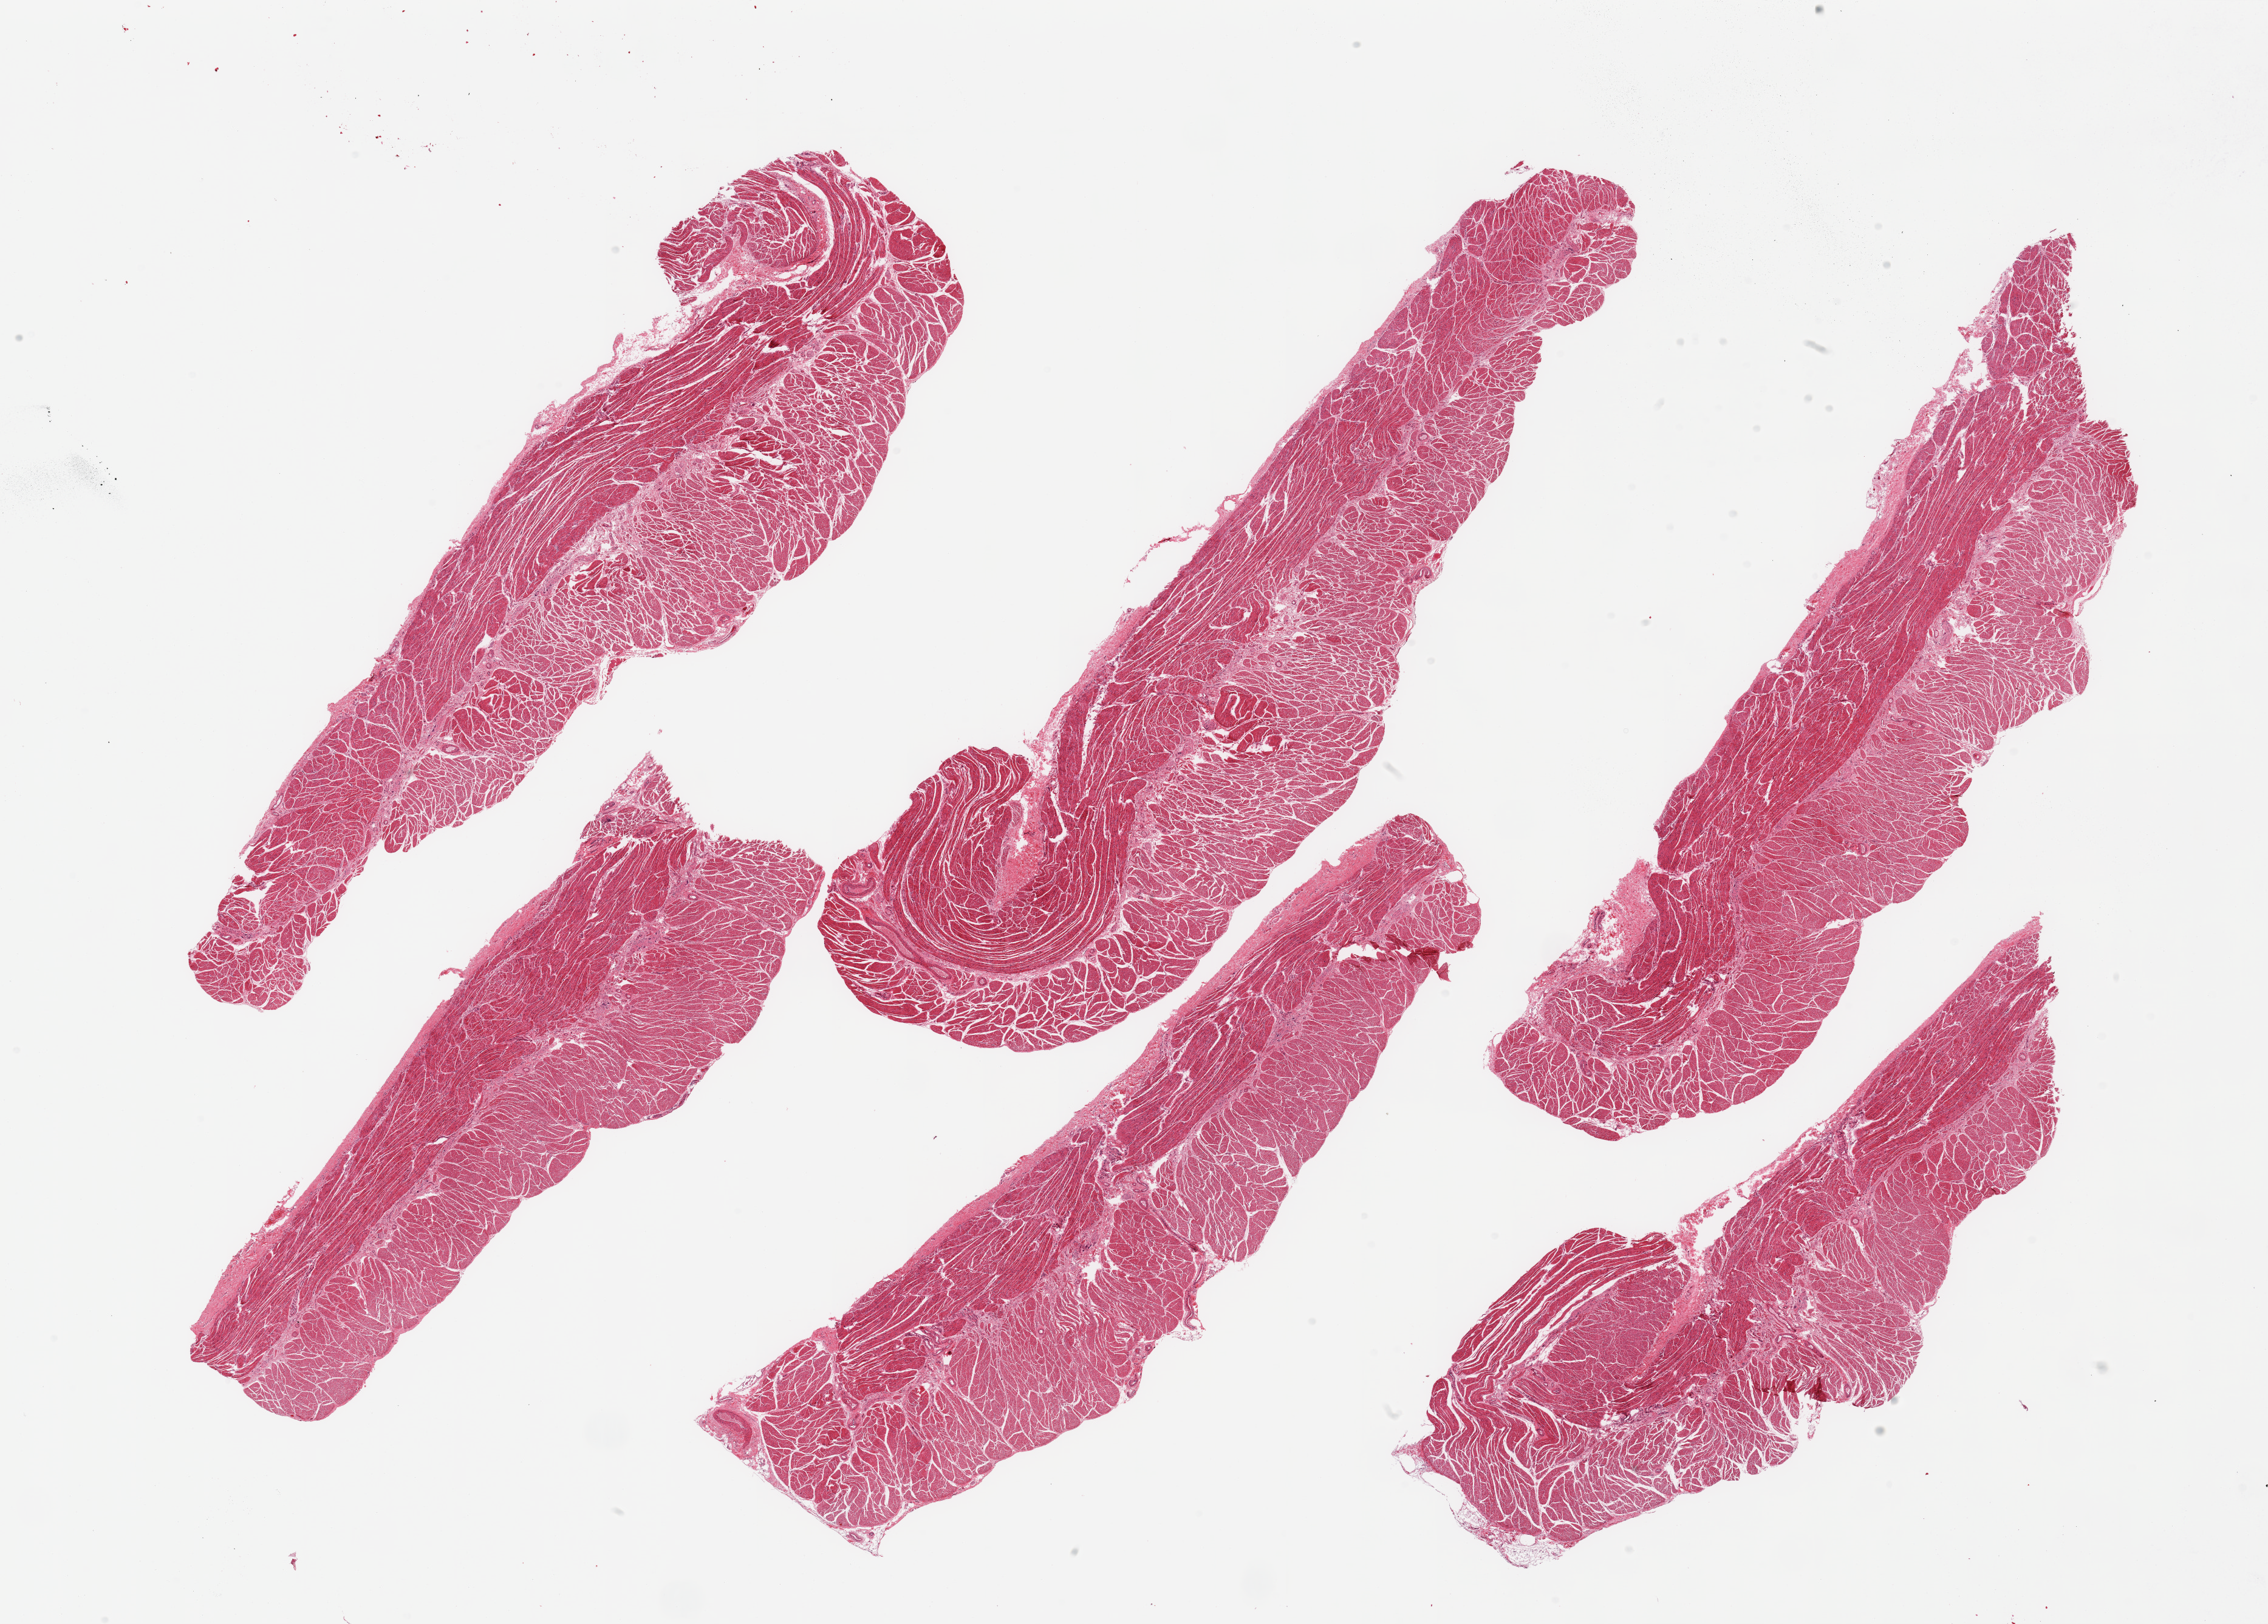
Whole-slide image, hematoxylin and eosin (H&E) stain — low-resolution overview of the scanned area, about 29.5 x 21.1 mm; PAXgene-fixed paraffin-embedded (PFPE) section; section of esophageal muscle (target tissue); tissue donor sample. Donor: male.
• review note (as recorded): 6 pieces; well trimmed target muscularis